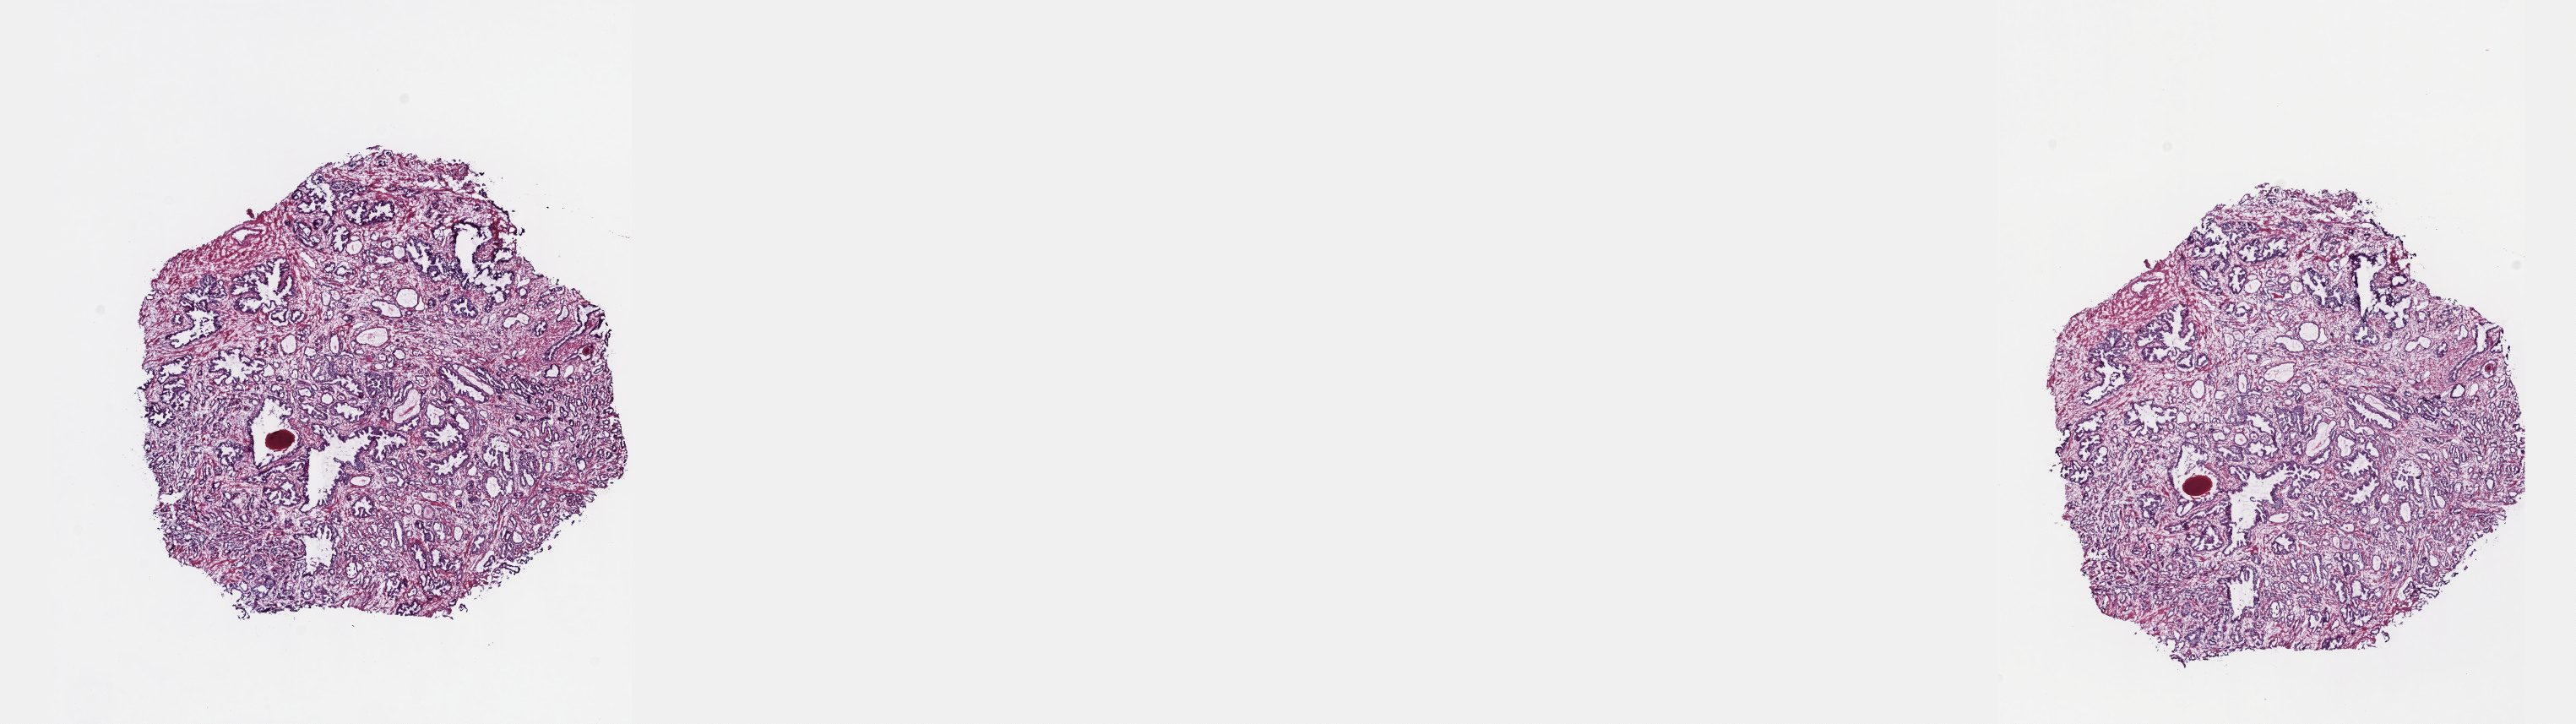
Digitized H&E tissue section (whole slide) — a low-resolution overview of the entire scanned area, about 24.6 x 6.9 mm (slide scanned at 40x); frozen section from the top of the tissue portion; prostate, primary tumour sample. Patient: male, age at initial diagnosis 51 years. Gleason score: 6 (3+3). Pathologist review of this section (percent, as recorded): tumour cells 45%, tumour nuclei 65%, normal cells 15%, stromal cells 40%, necrosis 0%. Inflammatory infiltration, as recorded: lymphocyte infiltration 0%, monocyte infiltration 0%, neutrophil infiltration 0%.
- lymph nodes positive (case pathology): 0 of 15 examined
- histologic diagnosis: Adenocarcinoma, NOS (prostate gland)